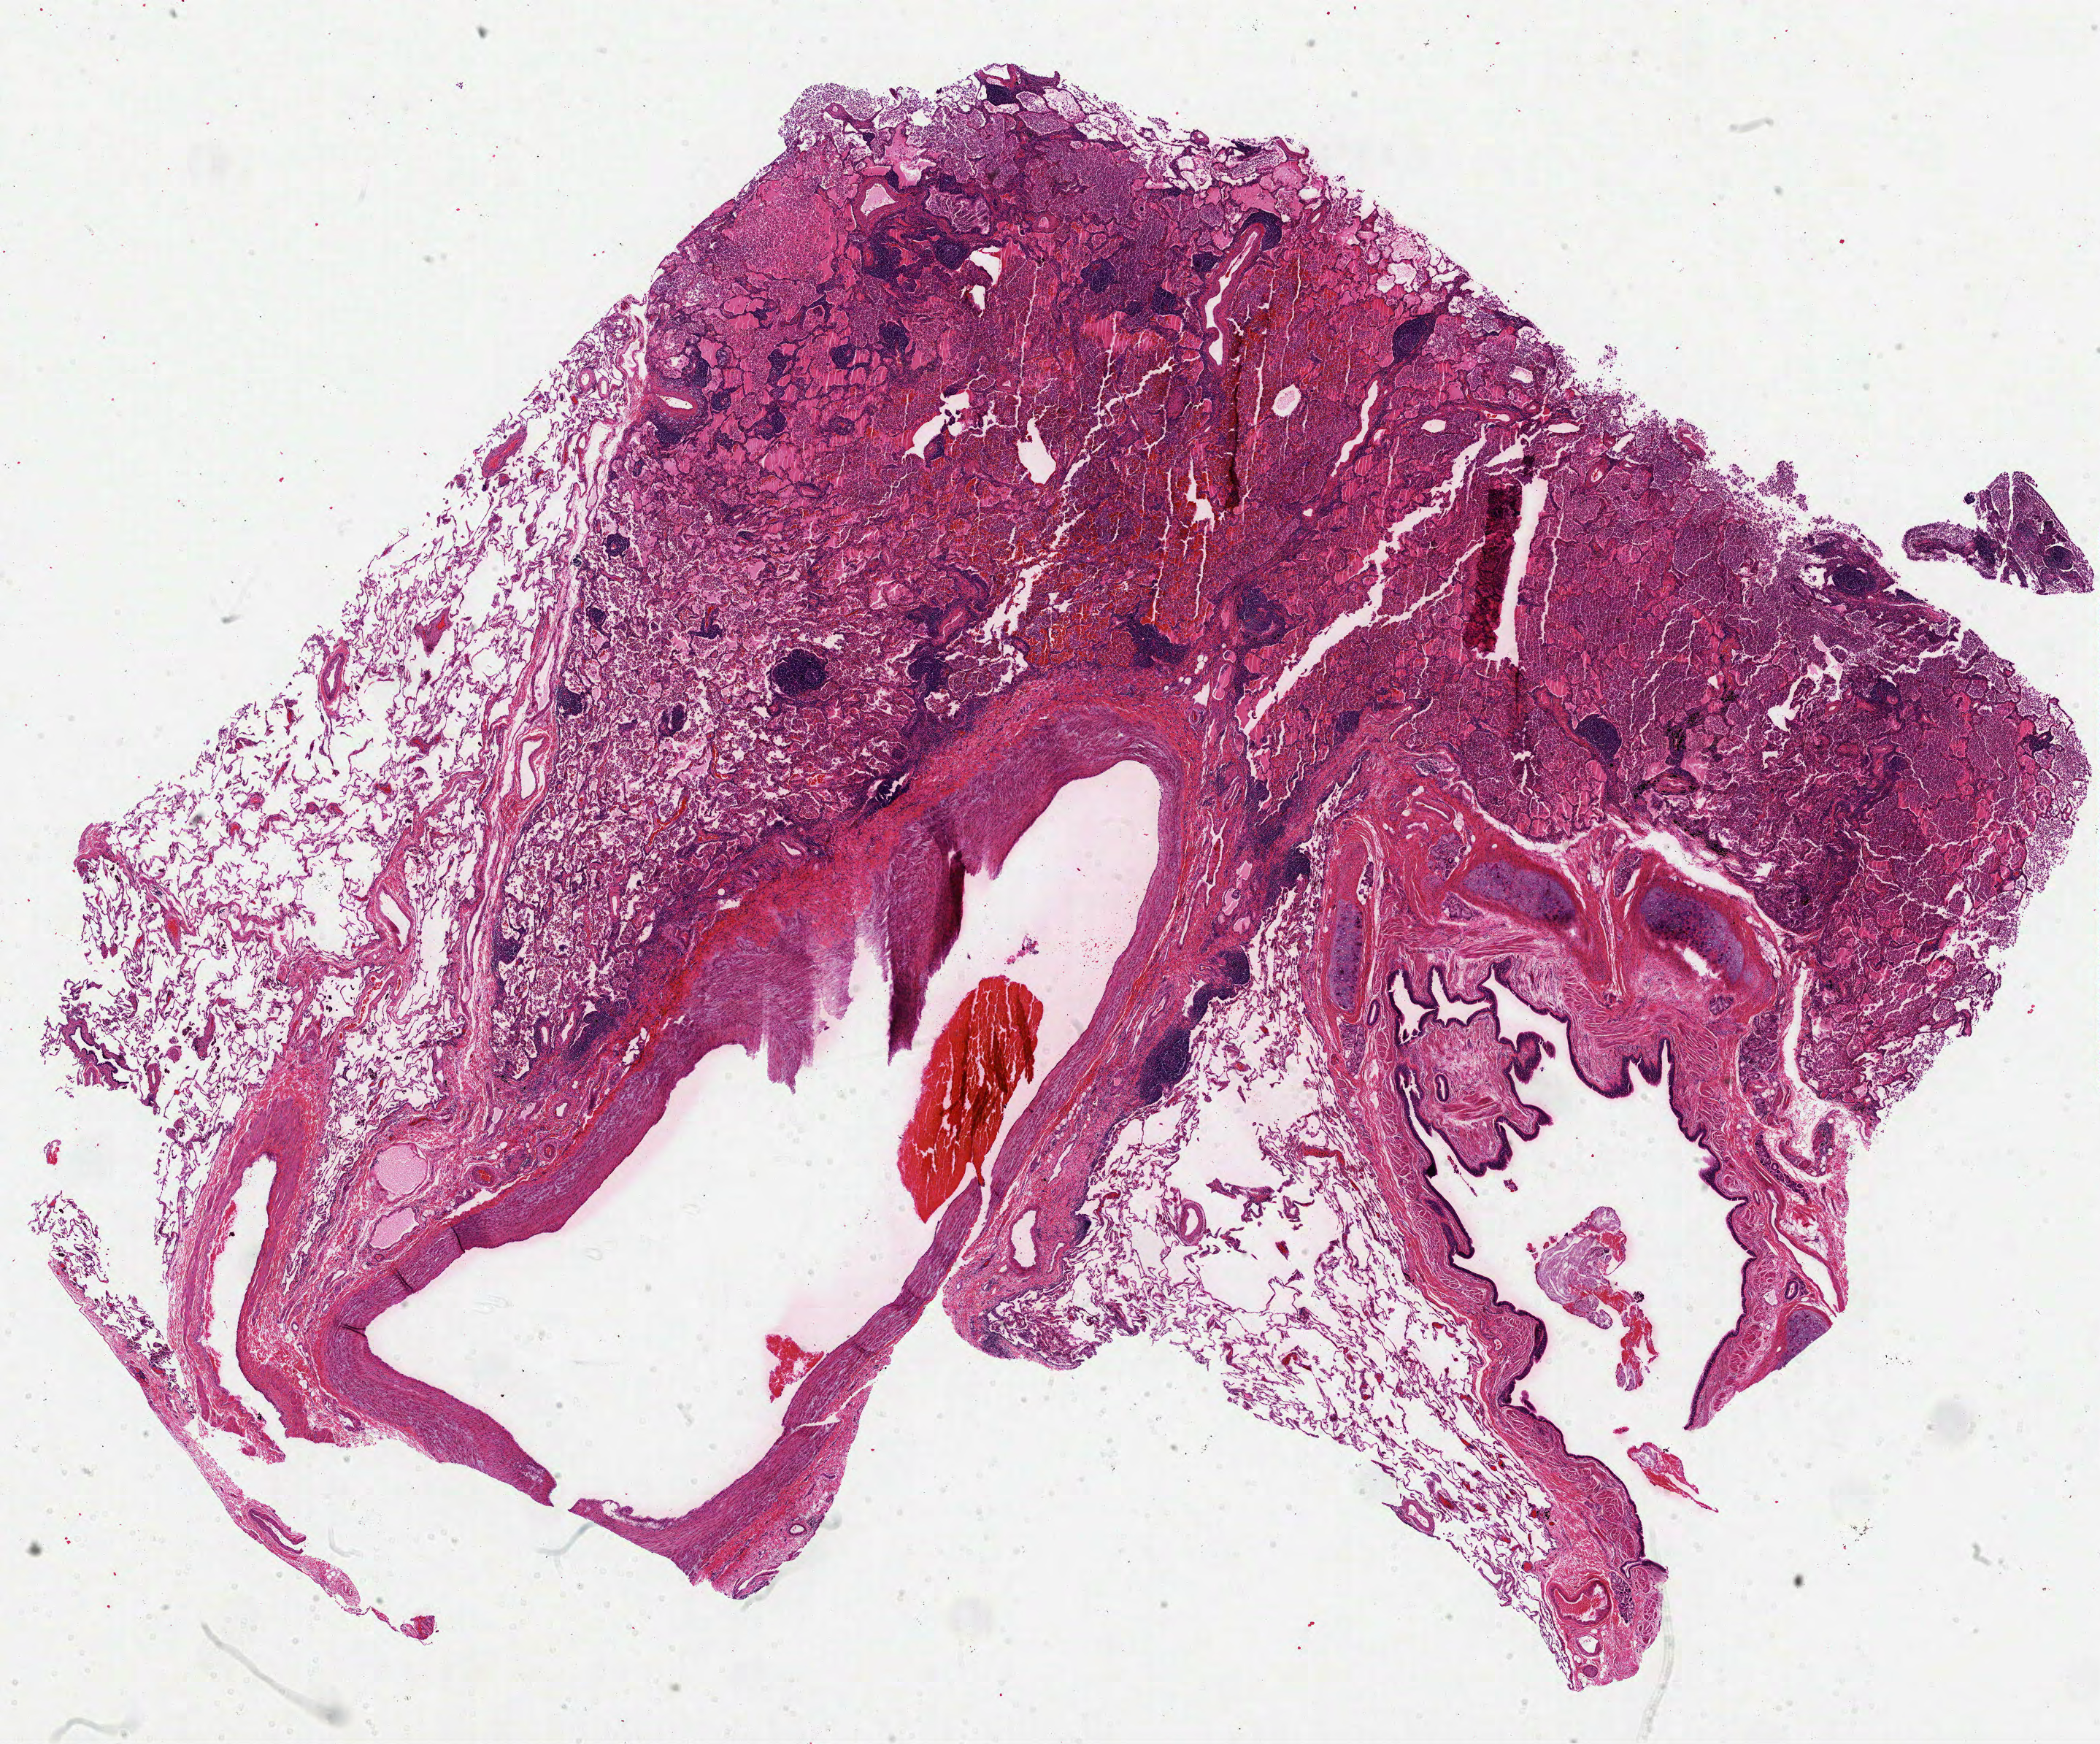
H&E whole-slide image — whole scanned area (about 23.2 x 19.3 mm) shown as a low-resolution overview. FFPE section. Primary tumour sample from the lung. Female, age 79 years at initial diagnosis.
Diagnosis: Papillary adenocarcinoma, NOS (upper lobe, lung). TNM: T1 N0 M0. AJCC pathologic stage: IA (6th edition).